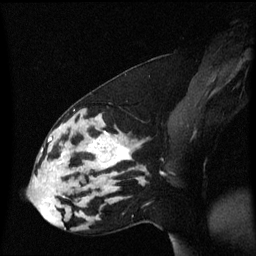
Breast MRI (dynamic contrast-enhanced), one sagittal slice. Position 24 of 60 along the scan axis. Dynamic contrast-enhanced series, image 2 of 3 at this slice position (ordered by acquisition). 1.5 T. TE 4.2 ms, TR 8.4 ms. 2 mm slice thickness. 256 × 256 image matrix, field of view 210 × 210 mm. Patient: female, 33 years. From the clinical record (not read from this slice): setting: breast cancer imaged before/during neoadjuvant chemotherapy; receptor status: triple-negative.
Structures marked on this image (semi-automatic segmentation, software-assisted and operator-edited):
- analysis volume of interest (the breast-tissue region the enhancement analysis was run in; not a lesion): bounding box (x1, y1, x2, y2) in pixels: (44, 123, 139, 189)
- tumour enhancement mask (voxels above the 70 % enhancement threshold inside the analysis volume of interest): (62, 133, 131, 170)